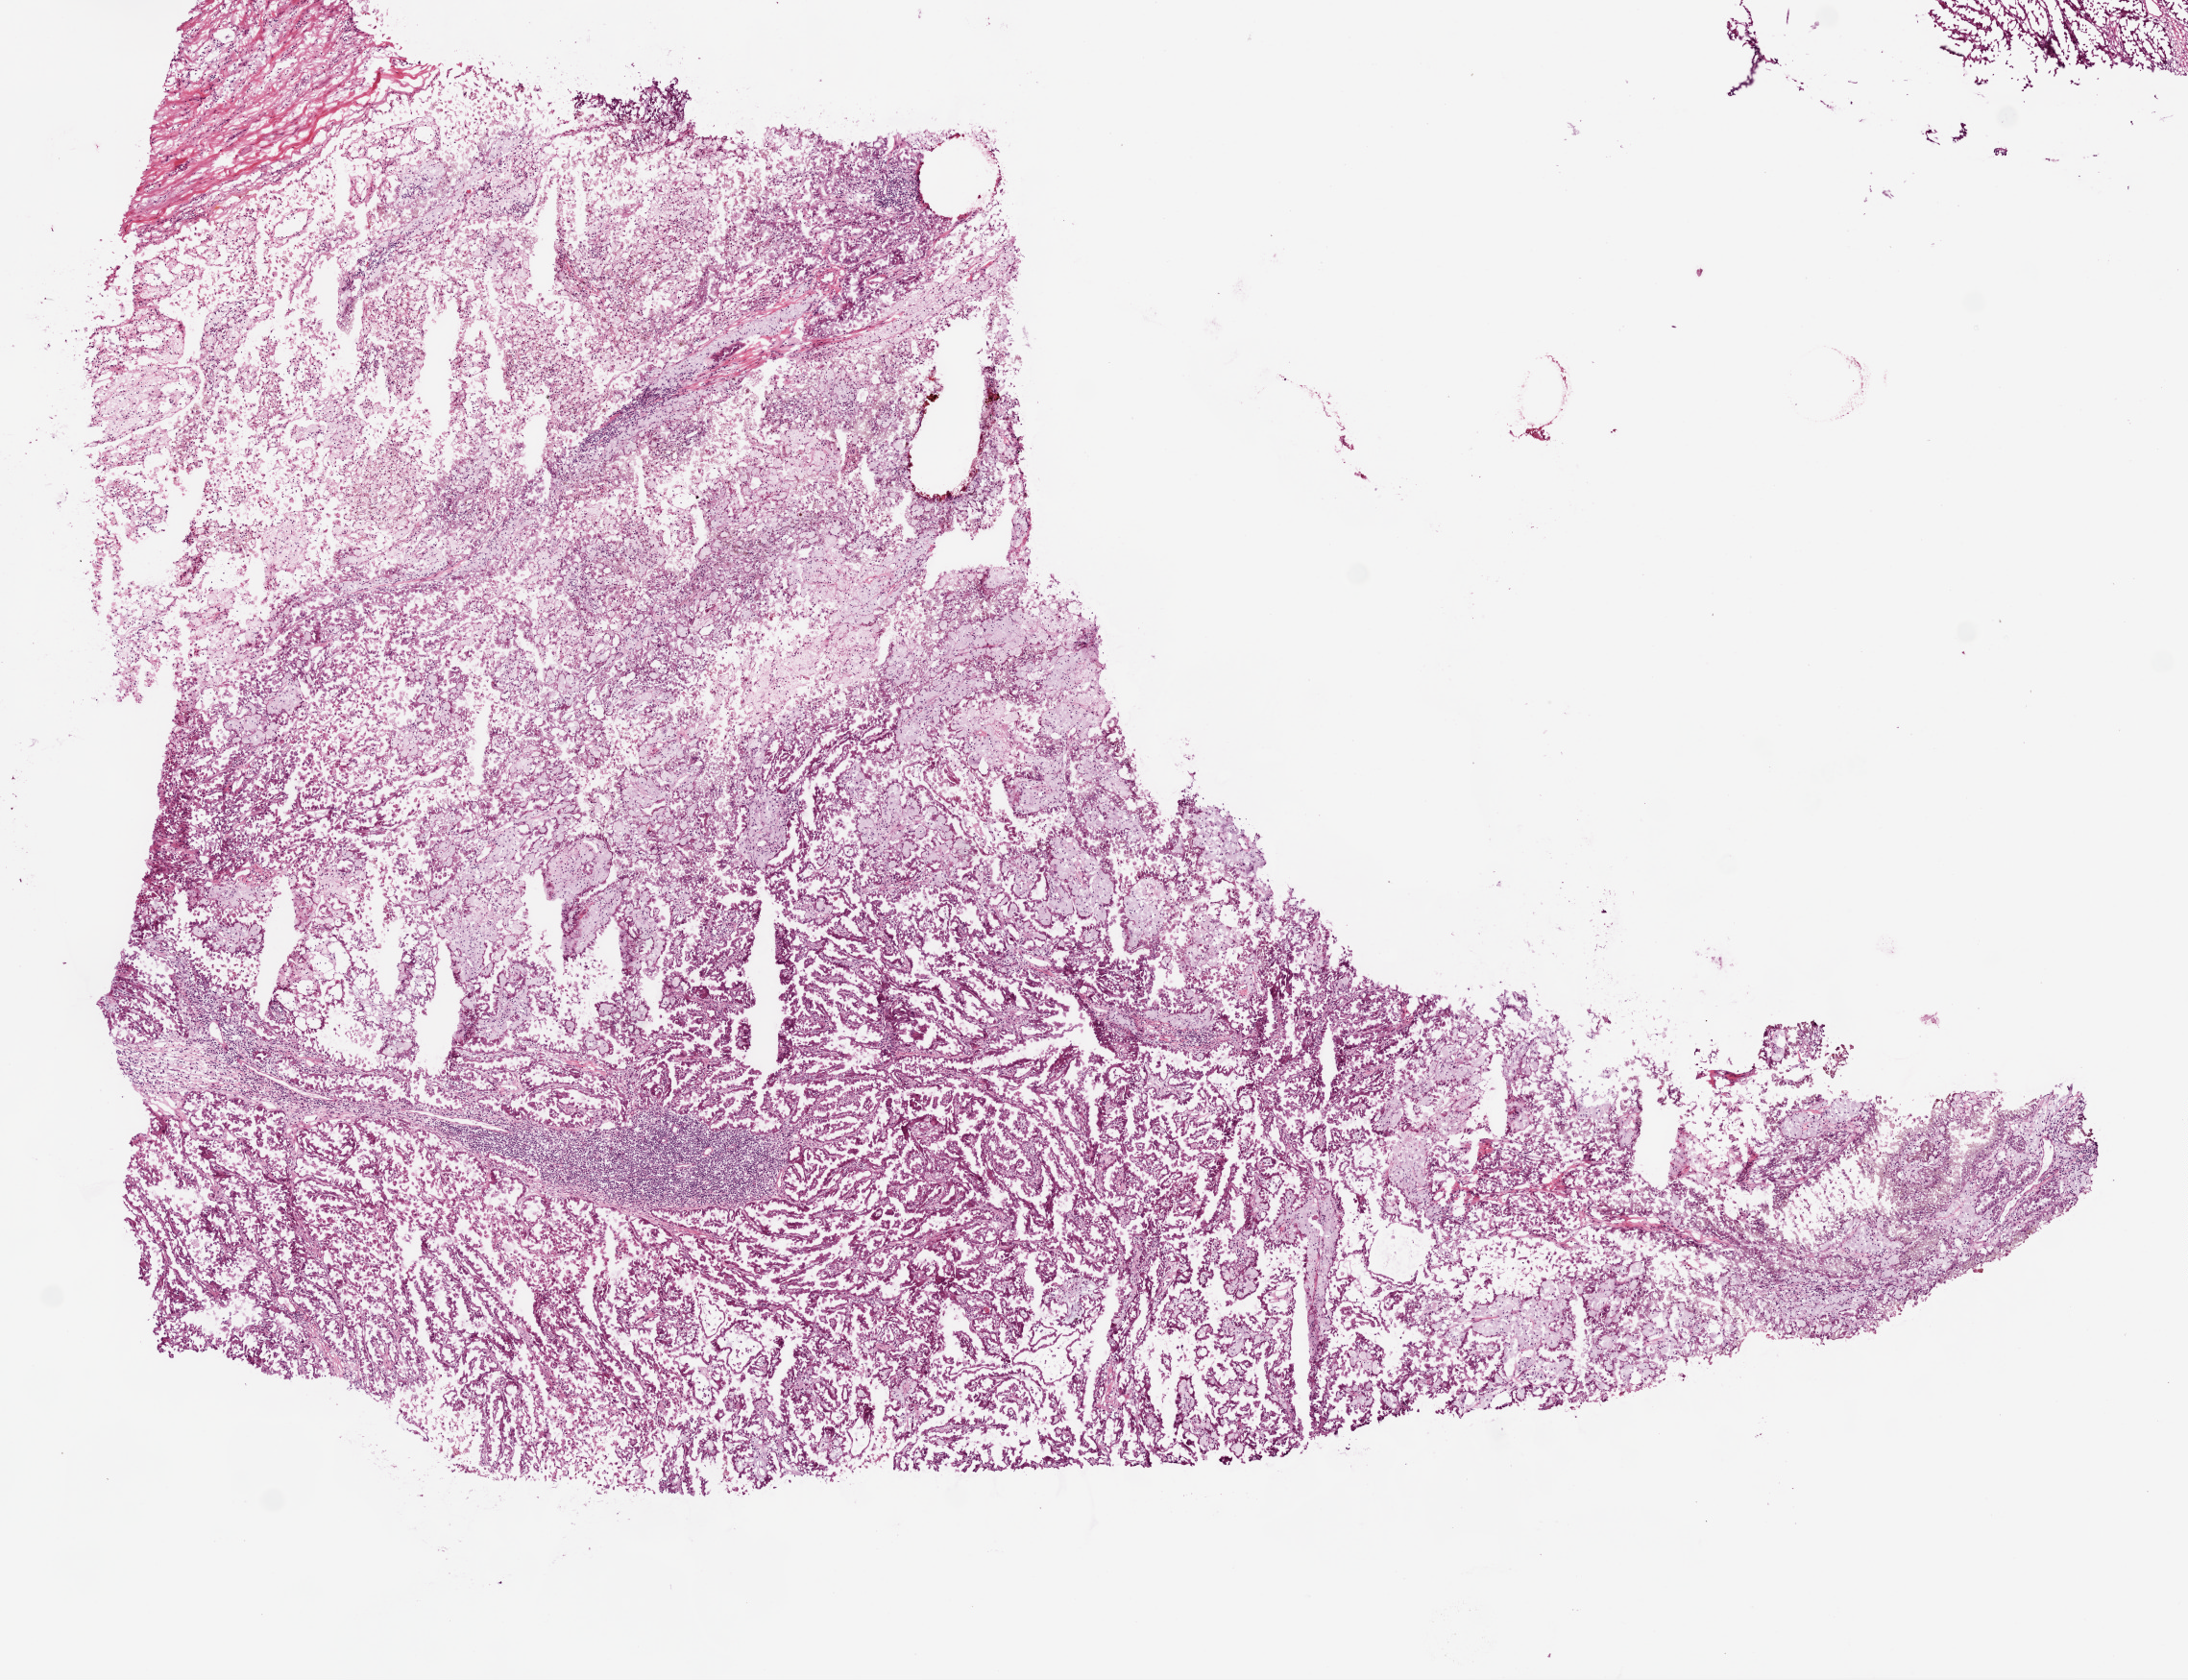
Digitized H&E-stained tissue section (whole slide) — whole scanned area (about 9.2 x 7.1 mm, slide scanned at 20x) shown as a low-resolution overview, frozen section, sample: primary tumour, kidney. Patient: male, age at initial diagnosis 78 years. Slide review estimates, as recorded: tumour cells 90%, tumour nuclei 75%.
Diagnosis: Papillary adenocarcinoma, NOS.